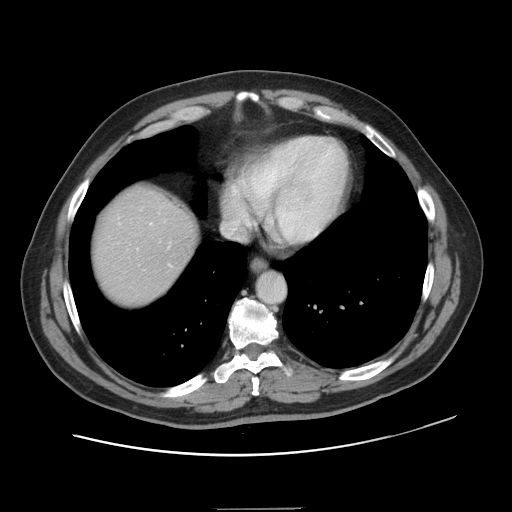
Contrast-enhanced abdominal CT, one axial slice. Slice 134 of 143 in the series (ordered by position). Soft-tissue window (W 400 / L 40 HU). 512 × 512 image matrix, field of view 402 × 402 mm. Male patient, age 62 years. Case-level facts recorded for this patient, not image findings: diagnosis: colorectal cancer liver metastases, imaged before liver resection; multiple liver metastases: yes; largest metastasis: 2.7 cm.
Outlined on this slice (expert manual segmentation):
- liver: bounding box <94,189,193,306> (left, top, right, bottom; pixels)
- planned liver remnant (the part of the liver to remain after resection): <94,190,193,300>